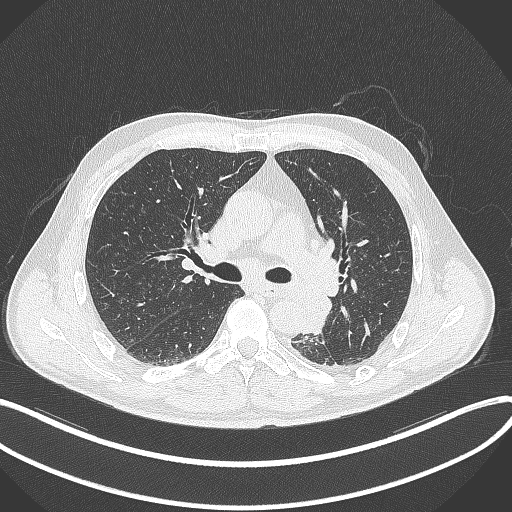
Chest CT, one axial slice. Position 211 of 329 along the scan axis. Lung window (W 1500 / L -600 HU). 512 × 512 image matrix. Male patient, age 59 years. Case-level facts recorded for this patient, not image findings: clinical TNM (as recorded): T2a N2 M0.
Structures marked on this image (rectangle marked by the reading radiologist):
- lung tumour (recorded histology: squamous cell carcinoma): bounding box <297,286,336,336> (left, top, right, bottom; pixels)